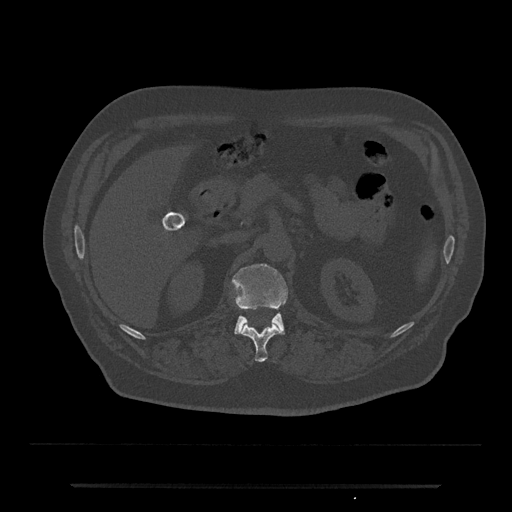
CT including the spine, one axial slice; position 564 of 797 along the scan axis; 120 kVp; bone window (W 1800 / L 400 HU); 512 × 512 image matrix, field of view 434 × 434 mm. Male patient, age 80 years. Case-level facts recorded for this patient, not image findings: primary cancer: prostate; vertebrae with lytic lesions (as recorded): L1, T11.
Structures marked on this image (semi-automatically segmented with operator editing):
- L1 vertebra: bounding box [x1, y1, x2, y2] px = [232, 263, 288, 335]
- T12 vertebra: [242, 324, 281, 362]